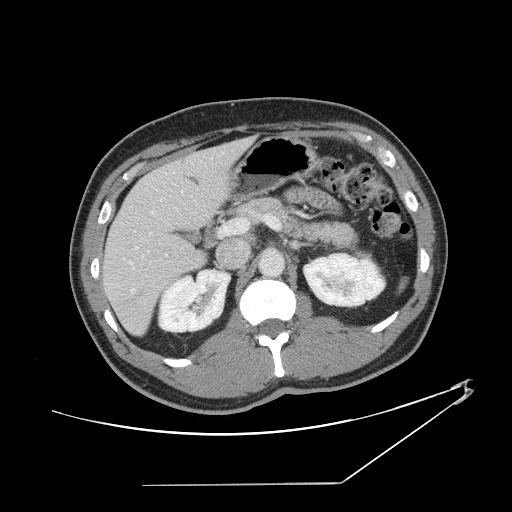
Contrast-enhanced abdominal CT, one axial slice. Slice 76 of 152 in the series (ordered by position). Reconstruction kernel STANDARD. Soft-tissue window (W 400 / L 40 HU). 512 × 512 image matrix, field of view 432 × 432 mm. Male patient, age 45 years. Case-level facts recorded for this patient, not image findings: diagnosis: colorectal cancer liver metastases, imaged before liver resection; multiple liver metastases: no; largest metastasis: 1 cm; disease in both lobes: no.
Outlined on this slice (outlined manually by an expert reader):
- hepatic veins: bounding box <131,152,224,292> (left, top, right, bottom; pixels)
- liver: <104,139,251,335>
- planned liver remnant (the part of the liver to remain after resection): <104,158,212,335>
- portal vein (with intrahepatic branches): <130,216,279,264>